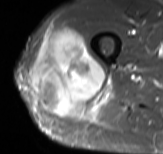
MRI of an extremity soft-tissue mass, one axial slice; slice 41 of 61 in the series (ordered by position); STIR; MR volume resampled by the dataset authors to the PET/CT grid (not the native acquisition matrix); 163 × 154 image matrix. Male patient. From the clinical record (not read from this slice): histological type: poorly differentiated synovial sarcoma; grade: high; site of the primary tumour: right buttock.
Annotated regions visible in this slice (expert contour drawn on MRI and transferred to this co-registered scan by the dataset authors):
- gross tumour volume including surrounding oedema: bounding box <30,27,108,118> (left, top, right, bottom; pixels)
- gross tumour volume (mass): <30,27,106,115>